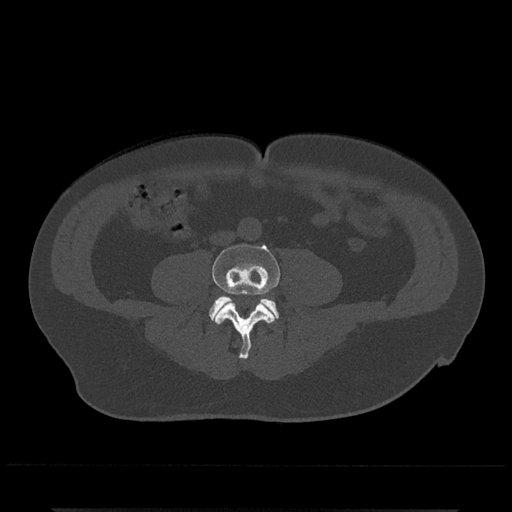
CT including the spine, one axial slice. Slice 137 of 797 in the series (ordered by position). Reconstruction kernel Br40s/3. 120 kVp. Bone window (W 1800 / L 400 HU). 512 × 512 image matrix. Patient: male, 67 years. Case-level facts recorded for this patient, not image findings: primary cancer: prostate.
Structures marked on this image (semi-automatically segmented with operator editing):
- L4 vertebra: bounding box <212,244,280,359> (left, top, right, bottom; pixels)
- L5 vertebra: <209,295,279,319>